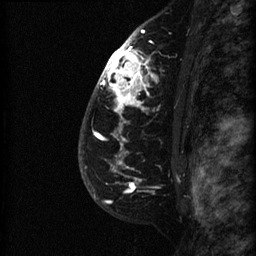
Breast MRI (dynamic contrast-enhanced), one sagittal slice. Slice 49 of 60 in the series (ordered by position). Dynamic contrast-enhanced series, image 2 of 3 at this slice position (ordered by acquisition). 1.5 T. TE 4.2 ms, TR 22.7 ms. 256 × 256 image matrix. Patient: female, 48 years. From the clinical record (not read from this slice): setting: breast cancer imaged before/during neoadjuvant chemotherapy; receptor status: triple-negative.
Outlined on this slice (semi-automatic segmentation, software-assisted and operator-edited):
- analysis volume of interest (the breast-tissue region the enhancement analysis was run in; not a lesion): bounding box <89,27,191,180> (left, top, right, bottom; pixels)
- tumour enhancement mask (voxels above the 90 % enhancement threshold inside the analysis volume of interest): <96,30,157,180>